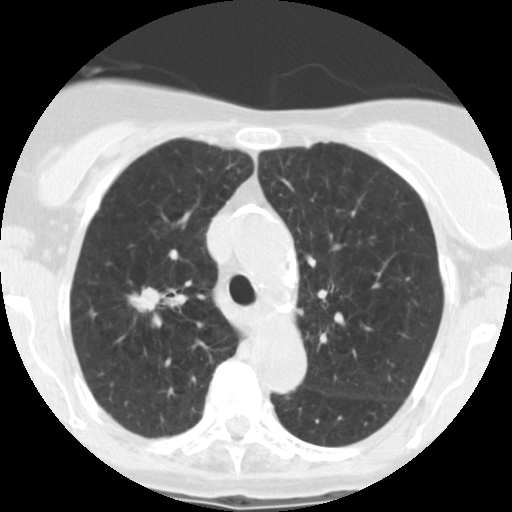
Low-dose screening chest CT, axial slice. First (baseline) screen. Lung window (W 1500 / L -600 HU). Standard (soft-tissue) reconstruction kernel (STANDARD). 120 kVp. Slice 178 of 246 in the series. Female participant, aged 67 years at enrolment. Former smoker at enrolment.
Expert reader's lesion annotation, bounding box <114,279,174,321> (left, top, right, bottom; pixels). The screening reader recorded 6 non-calcified nodules or masses ≥4 mm on this exam (right upper lobe, right middle lobe, left lower lobe, right middle lobe, left lower lobe, left lower lobe); which of them this box marks is not recorded. Official screen result: positive, change unspecified: nodule(s) >= 4 mm or enlarging nodule(s), mass(es), or other non-specific abnormalities suspicious for lung cancer. Participant outcome: lung cancer diagnosed 15 days after this screen — adenocarcinoma, NOS, right upper lobe, moderately differentiated (G2), stage IA (AJCC 6th edition), 14 mm at pathology.